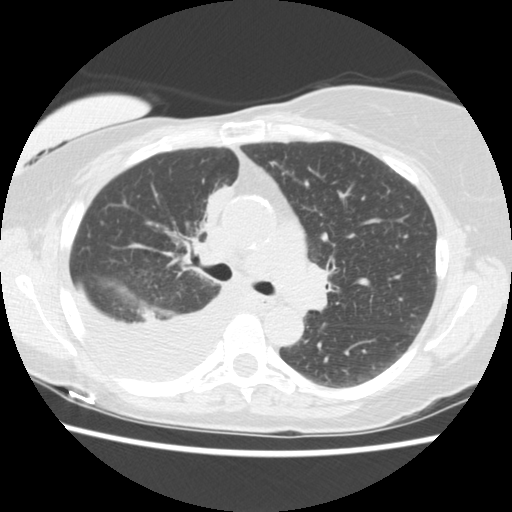
Low-dose screening chest CT, one axial slice; position 94 of 157 along the scan axis; reconstruction kernel STANDARD; lung window (W 1500 / L -600 HU); 2.5 mm slice thickness; 512 × 512 image matrix, field of view 330 × 330 mm.
Outlined on this slice (manually delineated by an expert):
- lesion 1 (tumor, upper lobe of right lung): bounding box [x1, y1, x2, y2] px = [204, 187, 233, 225]